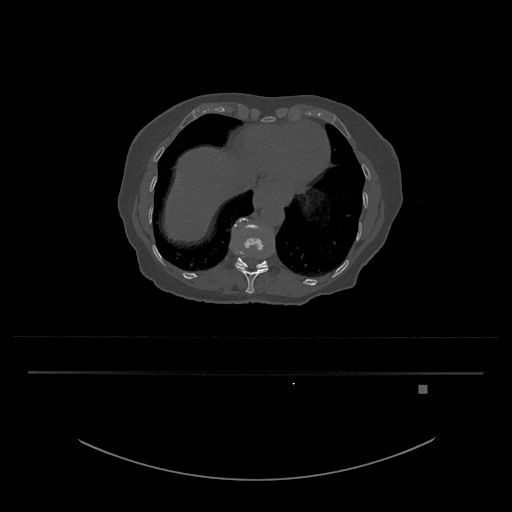
CT including the spine, one axial slice; slice 644 of 797 in the series (ordered by position); reconstruction kernel Br40s/3; 120 kVp; bone window (W 1800 / L 400 HU); 0.5 mm slice thickness; 512 × 512 image matrix, field of view 500 × 500 mm. Female patient, age 57 years. Case-level facts recorded for this patient, not image findings: primary cancer: cervical.
Outlined on this slice (semi-automatically segmented with operator editing):
- T11 vertebra: bounding box <235,264,268,294> (left, top, right, bottom; pixels)
- T12 vertebra: <234,218,269,270>